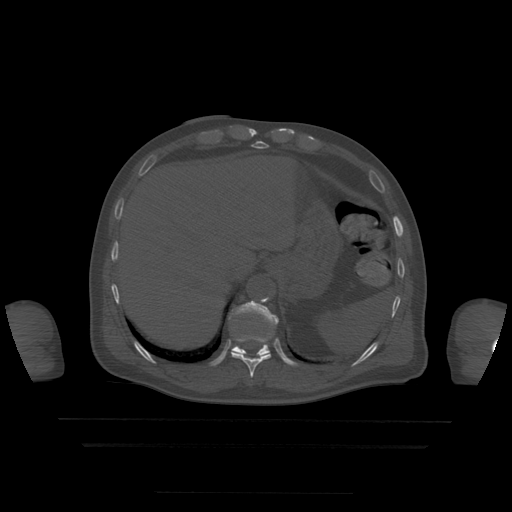
CT including the spine, one axial slice. Position 232 of 522 along the scan axis. Bone window (W 1800 / L 400 HU). 1.25 mm slice thickness. 512 × 512 image matrix, field of view 436 × 436 mm. Patient age 68 years. From the clinical record (not read from this slice): primary cancer: urothelial.
Structures marked on this image (semi-automatic segmentation, software-assisted and operator-edited):
- T10 vertebra: box from (x=231, y=310) to (x=271, y=378) px
- T11 vertebra: (x=230, y=301)–(x=279, y=357)